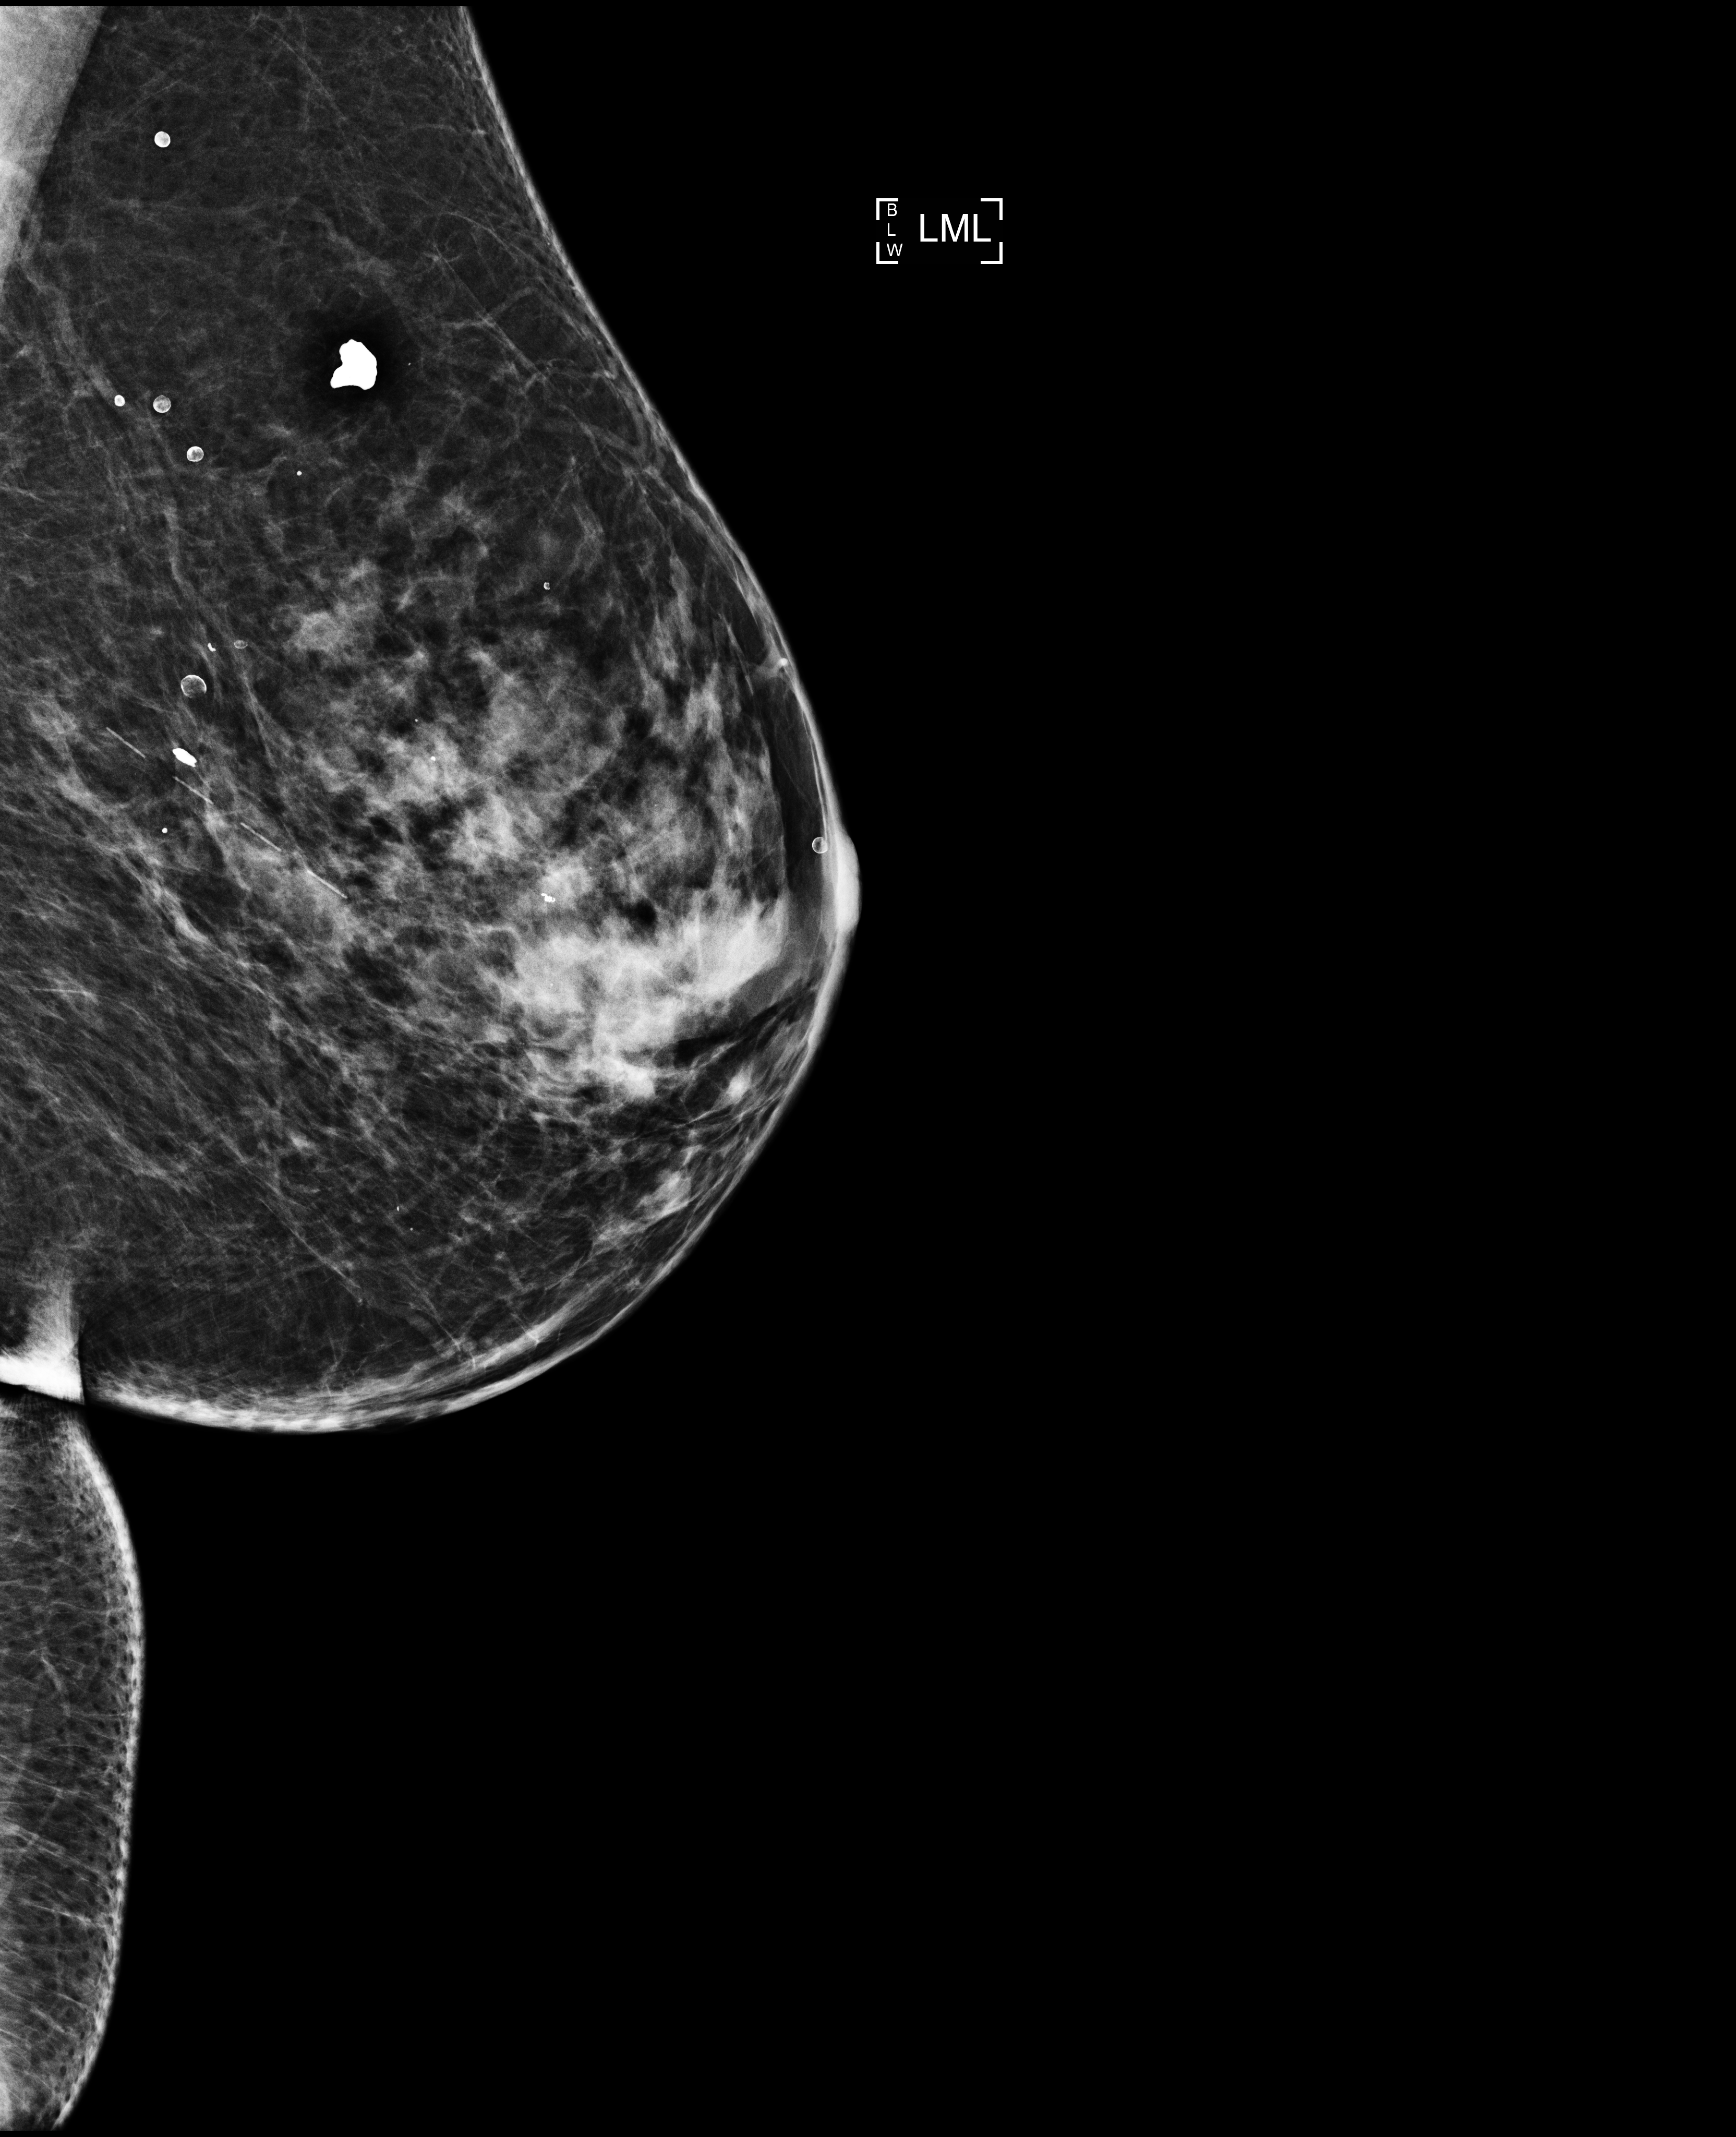
Diagnostic work-up study; compressed breast thickness 40 mm. Patient: female, 69 years.
Image type: full-field digital mammogram. Breast: left. Projection: mediolateral (ML) view.